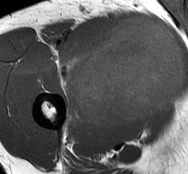
MRI of an extremity soft-tissue mass, one axial slice. Position 47 of 93 along the scan axis. MR volume resampled by the dataset authors to the PET/CT grid (not the native acquisition matrix). 188 × 174 image matrix, field of view 184 × 170 mm. Male patient. From the clinical record (not read from this slice): histological type: undifferentiated - pleiomorphic; grade: high; site of the primary tumour: right thigh.
Annotated regions visible in this slice (expert contour drawn on MRI and transferred to this co-registered scan by the dataset authors):
- gross tumour volume including surrounding oedema: bounding box [x1, y1, x2, y2] px = [63, 17, 185, 130]
- gross tumour volume (mass): [72, 19, 185, 129]